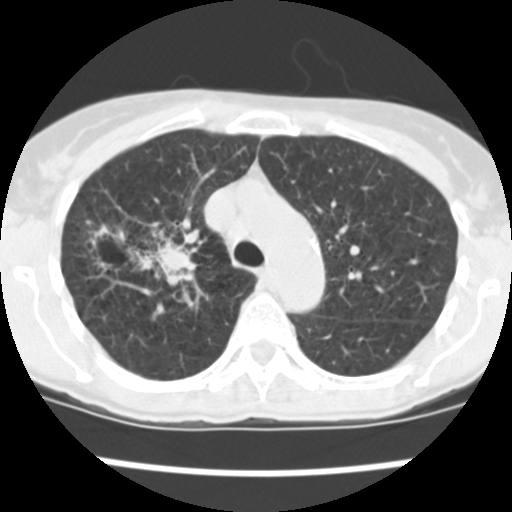
Chest CT (low-dose screening protocol), one axial image; baseline annual screen; lung window (W 1500 / L -600 HU); standard (soft-tissue) reconstruction kernel (STANDARD); slice 177 of 252 in the series. Female participant, aged 60 years at enrolment. Current smoker at enrolment.
- Lesion marked by an expert reader, bounding box <84,216,200,285> (left, top, right, bottom; pixels).
- The screening reader recorded 3 non-calcified nodules or masses ≥4 mm on this exam (right upper lobe, right upper lobe, right lower lobe); which of them this box marks is not recorded.
- Participant outcome: lung cancer diagnosed 19 days after this screen — non-small cell carcinoma, right upper lobe, stage IV (AJCC 6th edition), 26 mm at pathology.